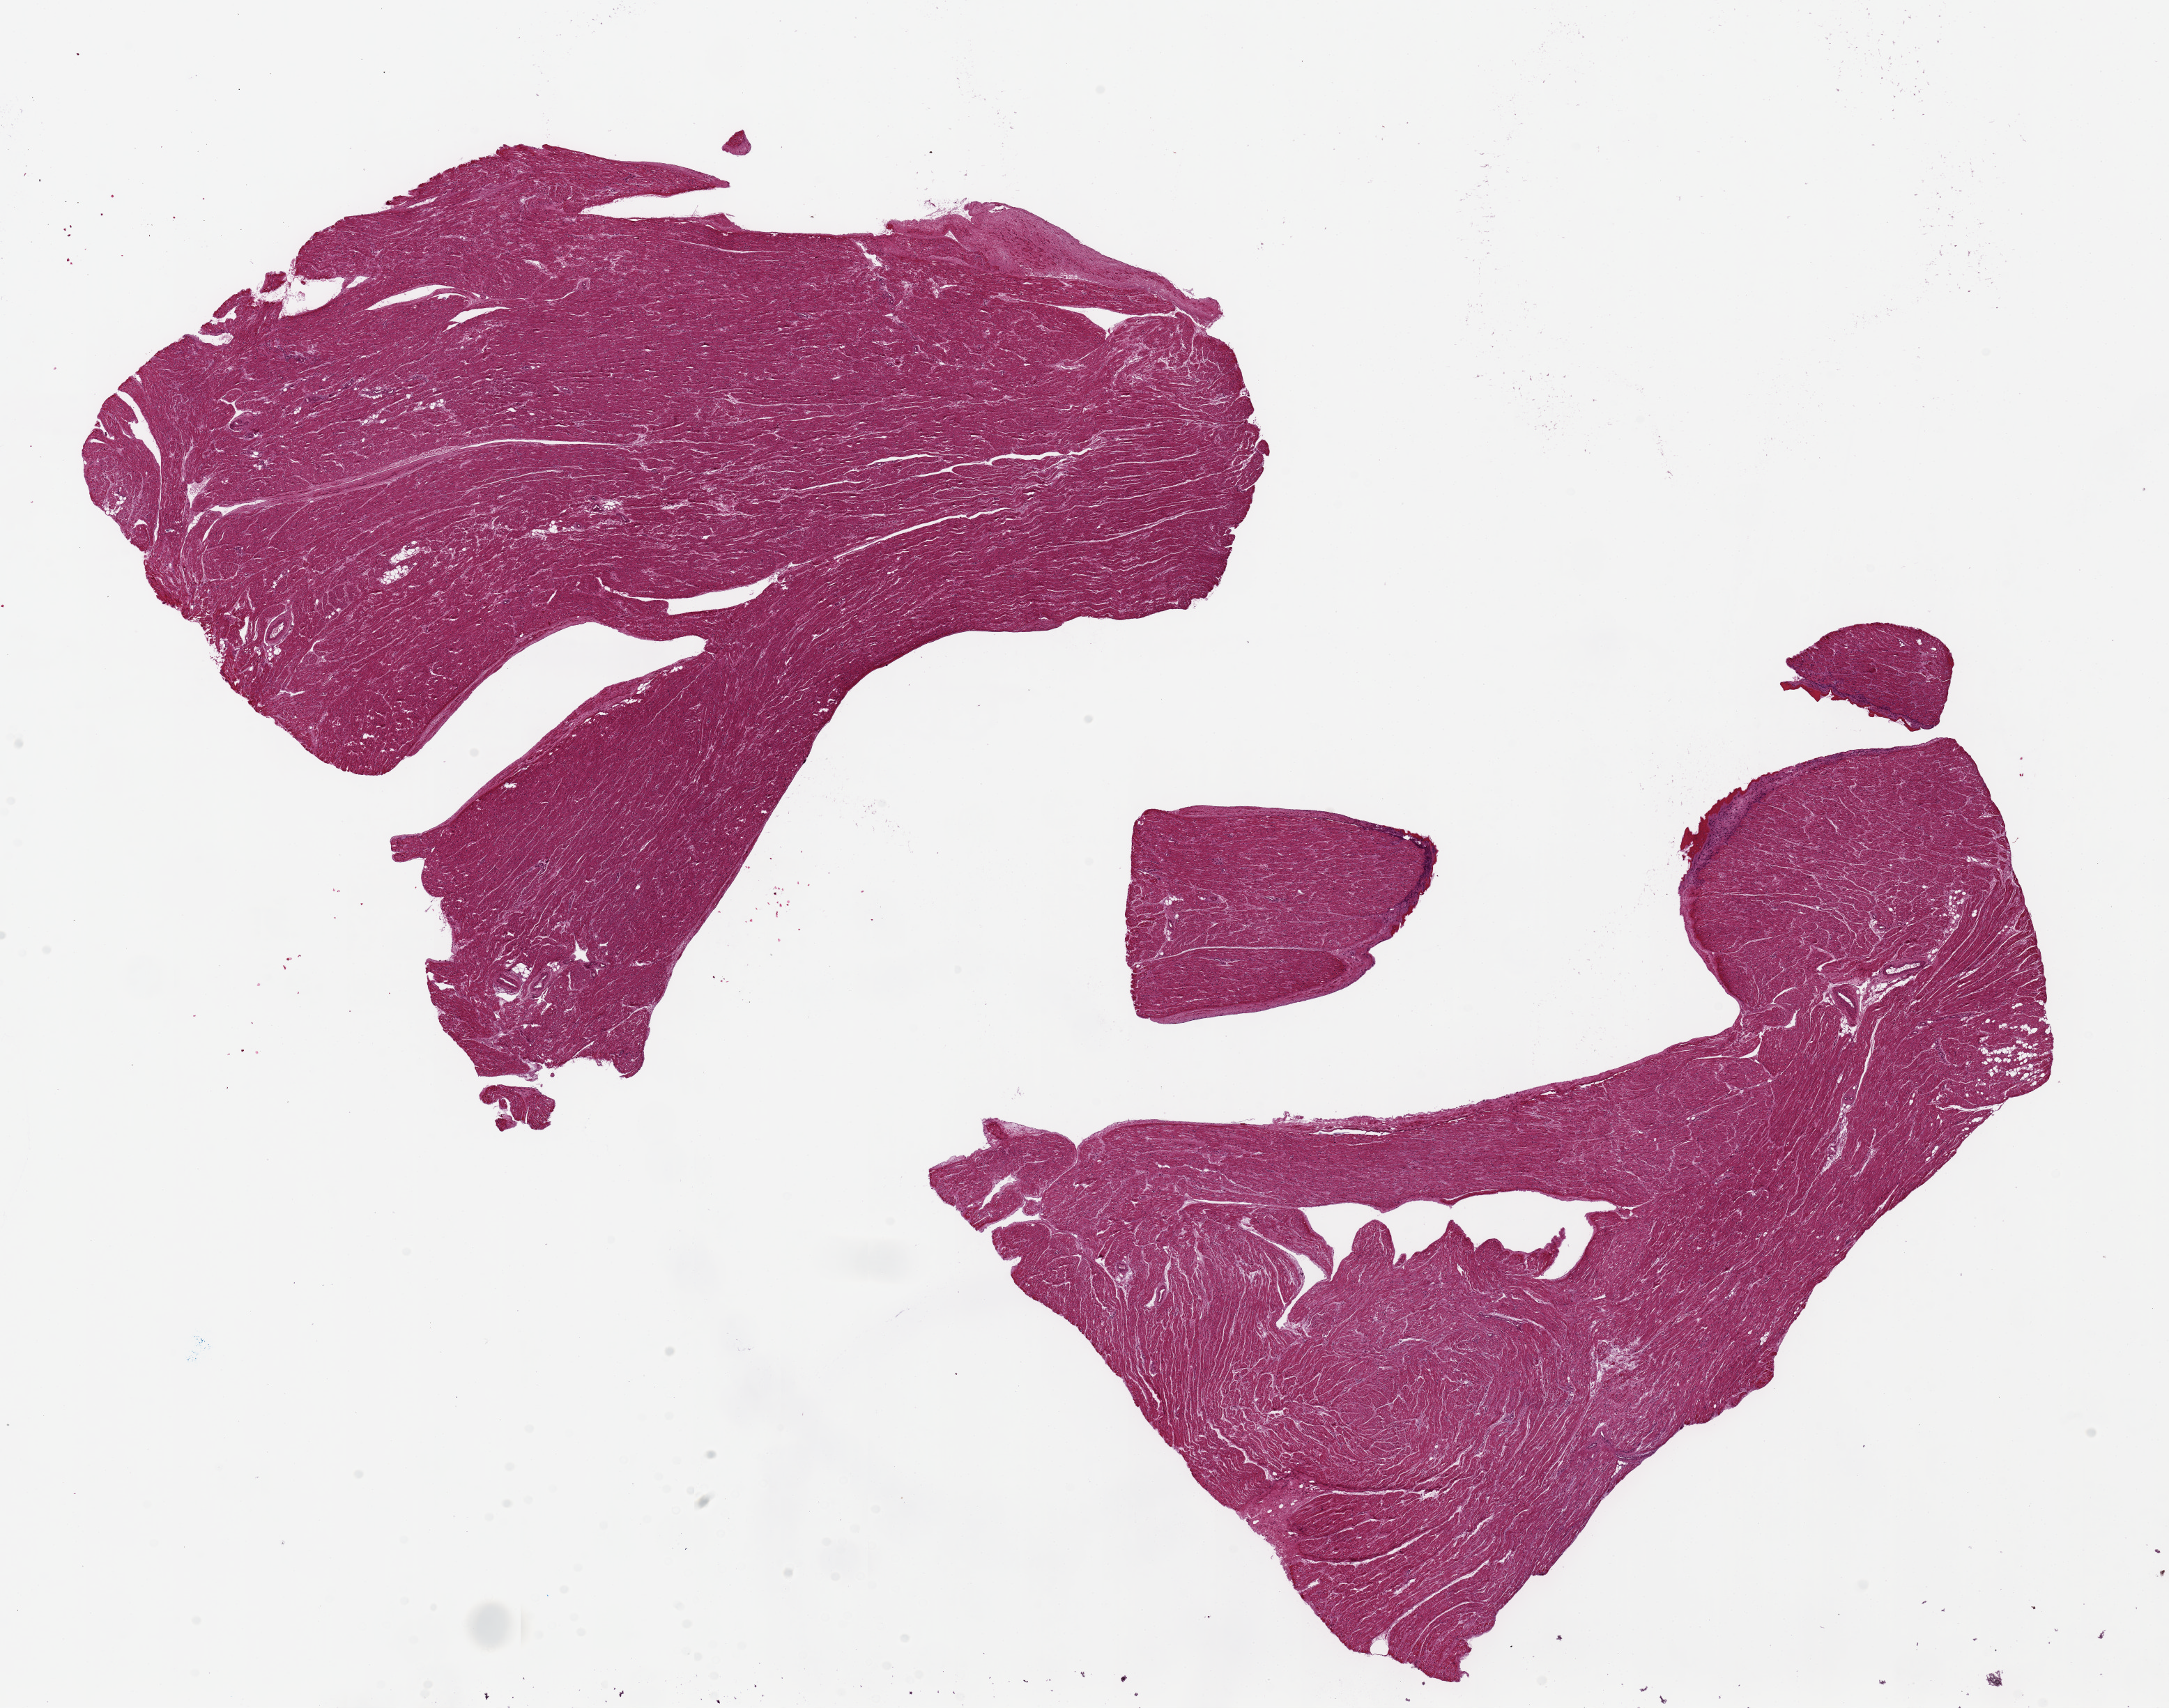
Haematoxylin and eosin whole-slide image, low-resolution overview of the scanned area, about 24.6 x 19.4 mm (acquisition: 20x scan); PAXgene-fixed paraffin-embedded (PFPE) section; target tissue: auricular appendage; tissue donor sample. Male donor.
- pathologist's review note for this sample: 2 pieces ~11x77